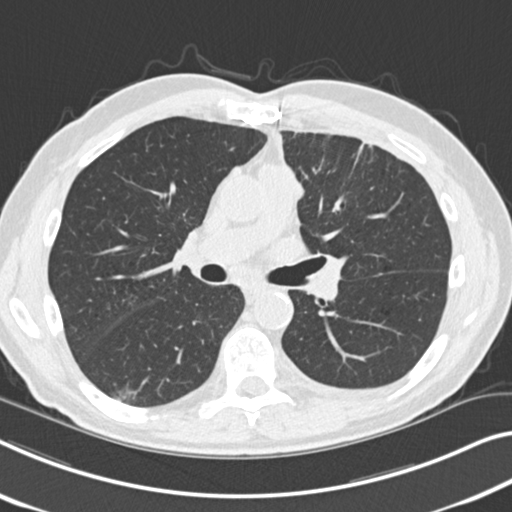
Axial slice from a low-dose chest CT screening exam. Baseline annual screen. Lung window (W 1500 / L -600 HU). 2 mm slice thickness. Slice 99 of 212 in the series. 512 × 512 image matrix. Male participant, aged 68 years at enrolment. Current smoker at enrolment.
• Lesion marked by an expert reader, bounding box <98,379,148,414> (left, top, right, bottom; pixels).
• Reader record for this screening exam (exam-level; its link to the box is not recorded): non-calcified nodule or mass ≥4 mm, right lower lobe, 14 × 10 mm, poorly defined margins, ground glass attenuation.
• Official screen result: positive, change unspecified: nodule(s) >= 4 mm or enlarging nodule(s), mass(es), or other non-specific abnormalities suspicious for lung cancer.